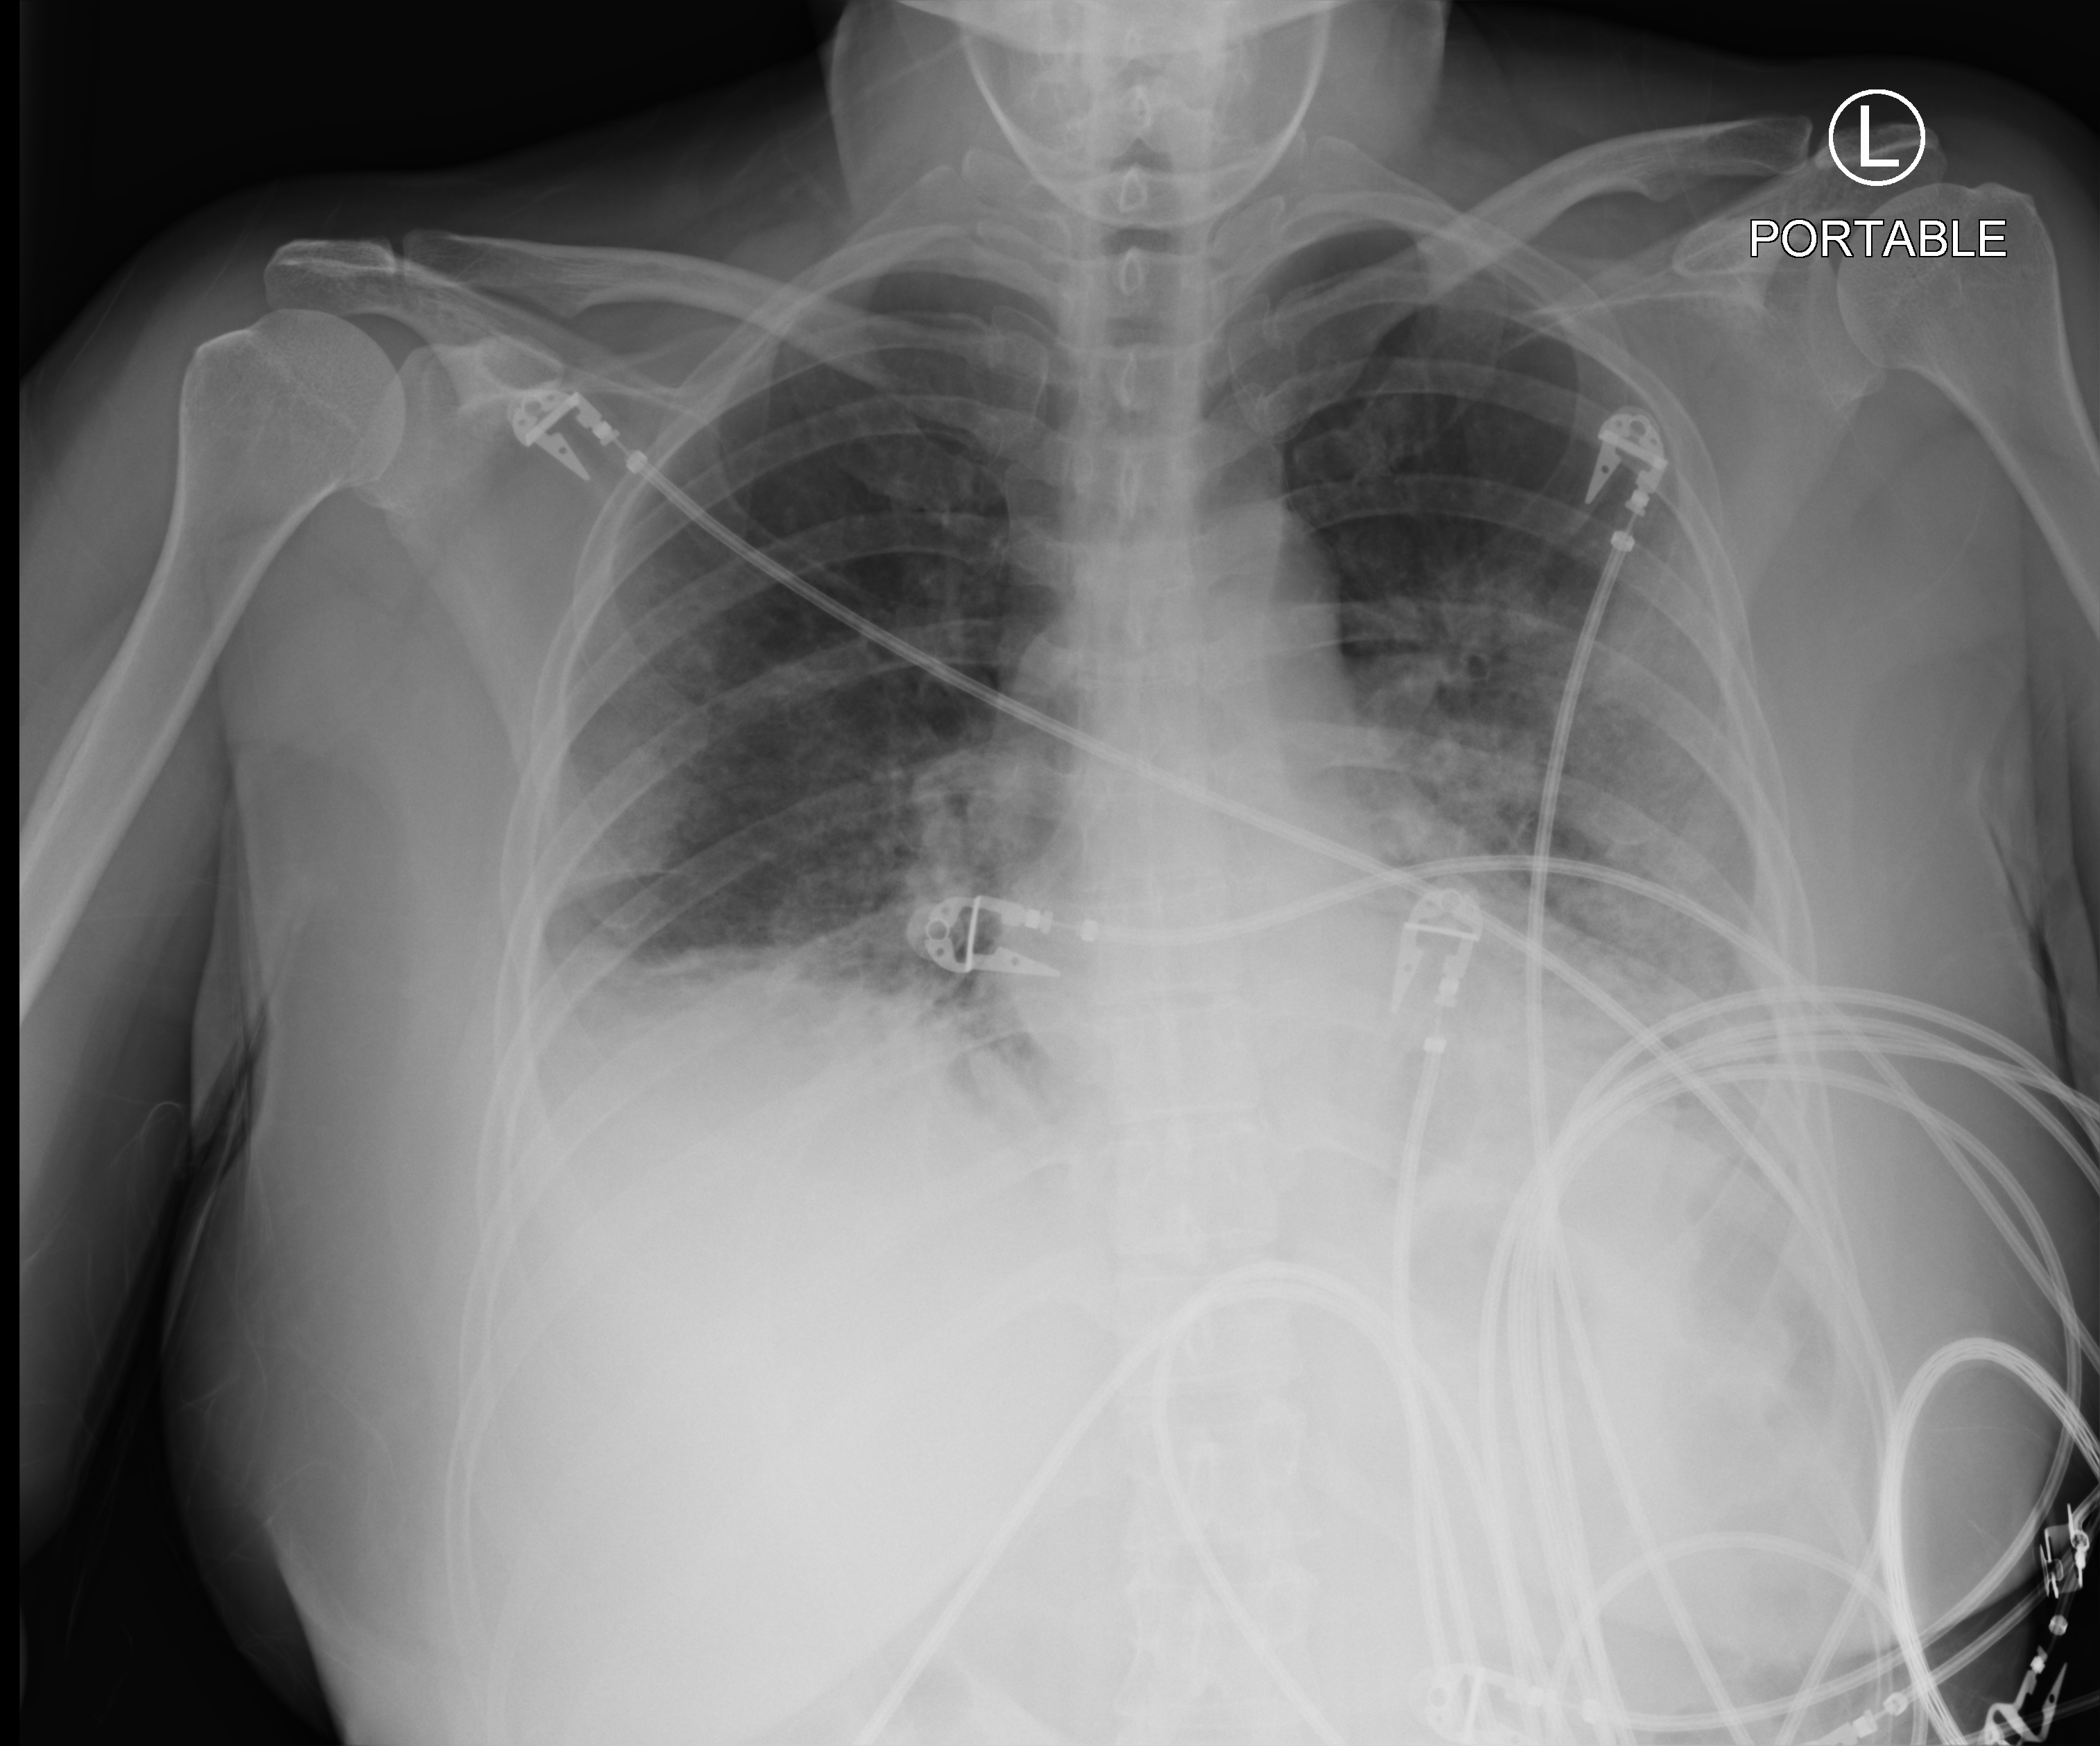
Bedside chest radiograph (computed radiography). Female patient hospitalised with COVID-19, age 18–59 years.
Hospital-stay facts (about this admission, not read from this image; timing relative to this image not recorded):
- diabetes (admission record): no